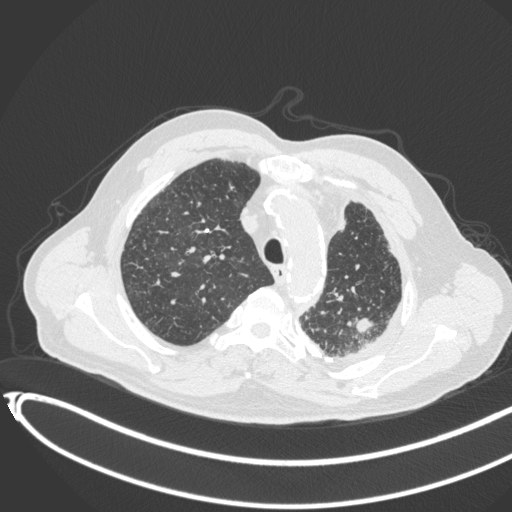
Chest CT, one axial slice; slice 336 of 451 in the series (ordered by position); reconstruction kernel B31f; 120 kVp; lung window (W 1500 / L -600 HU); 512 × 512 image matrix, field of view 400 × 400 mm. Patient: male, 78 years. From the clinical record (not read from this slice): clinical TNM (as recorded): T1c N0 M1.
Annotated regions visible in this slice (bounding box drawn by a radiologist):
- lung tumour (recorded histology: adenocarcinoma): bounding box <349,312,375,337> (left, top, right, bottom; pixels)